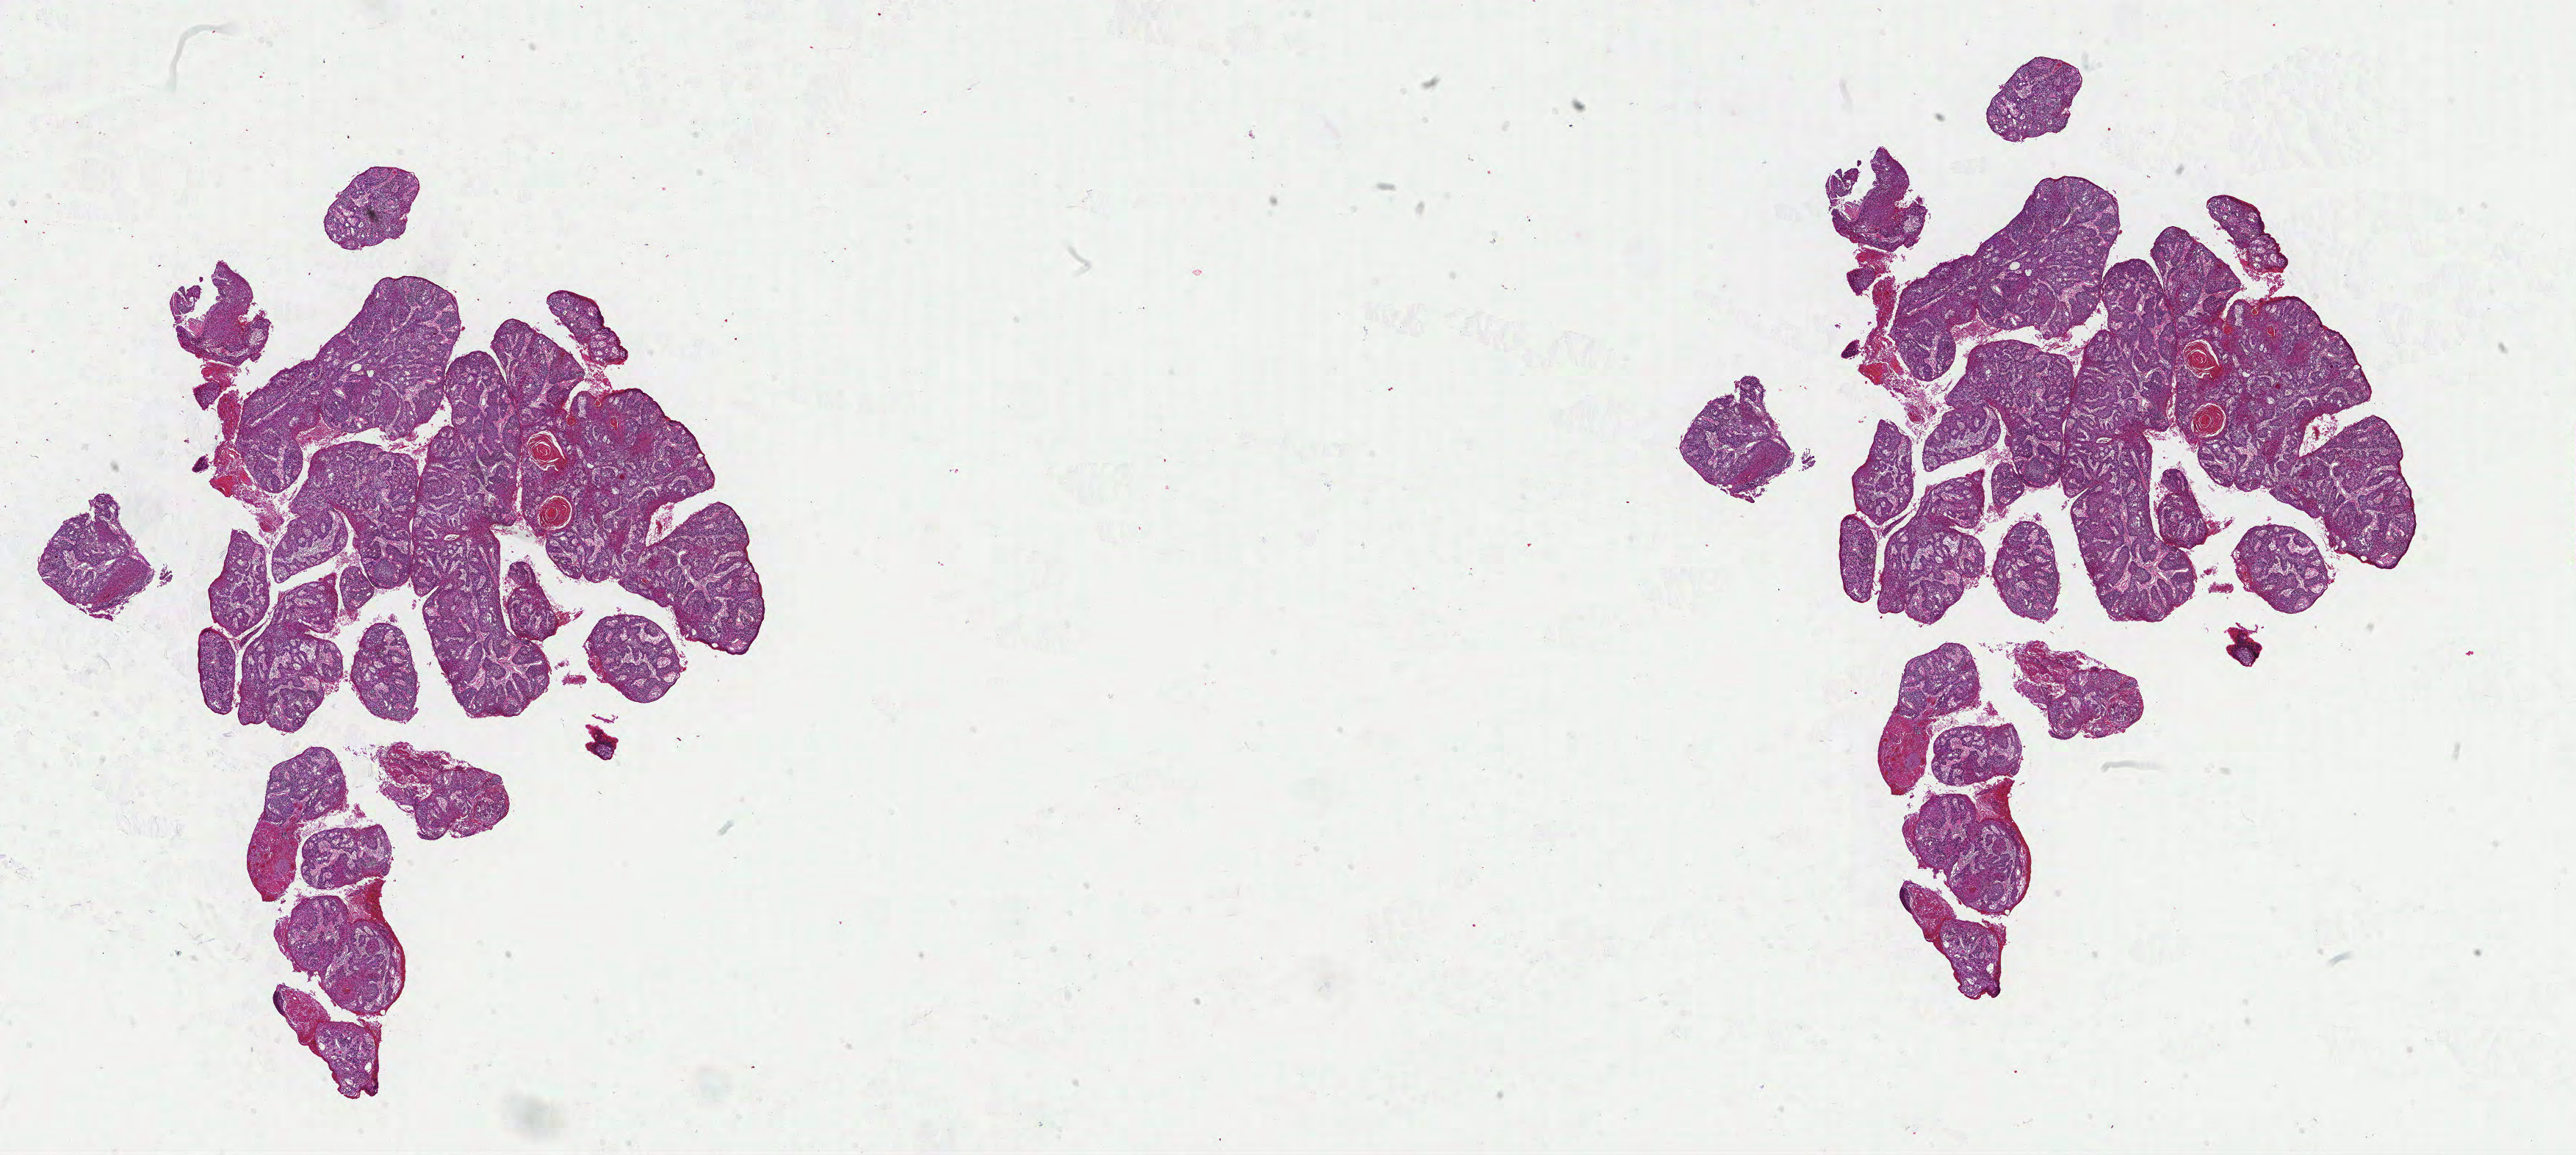
H&E-stained whole-slide image, a low-resolution overview of the entire scanned area, about 28.4 x 12.8 mm, FFPE section, head and neck, primary tumour sample. Male patient; age at initial diagnosis 53 years. Histologic grade: G2 (moderately differentiated).
- AJCC pathologic stage: III (7th edition)
- pathologic diagnosis: Squamous cell carcinoma, NOS